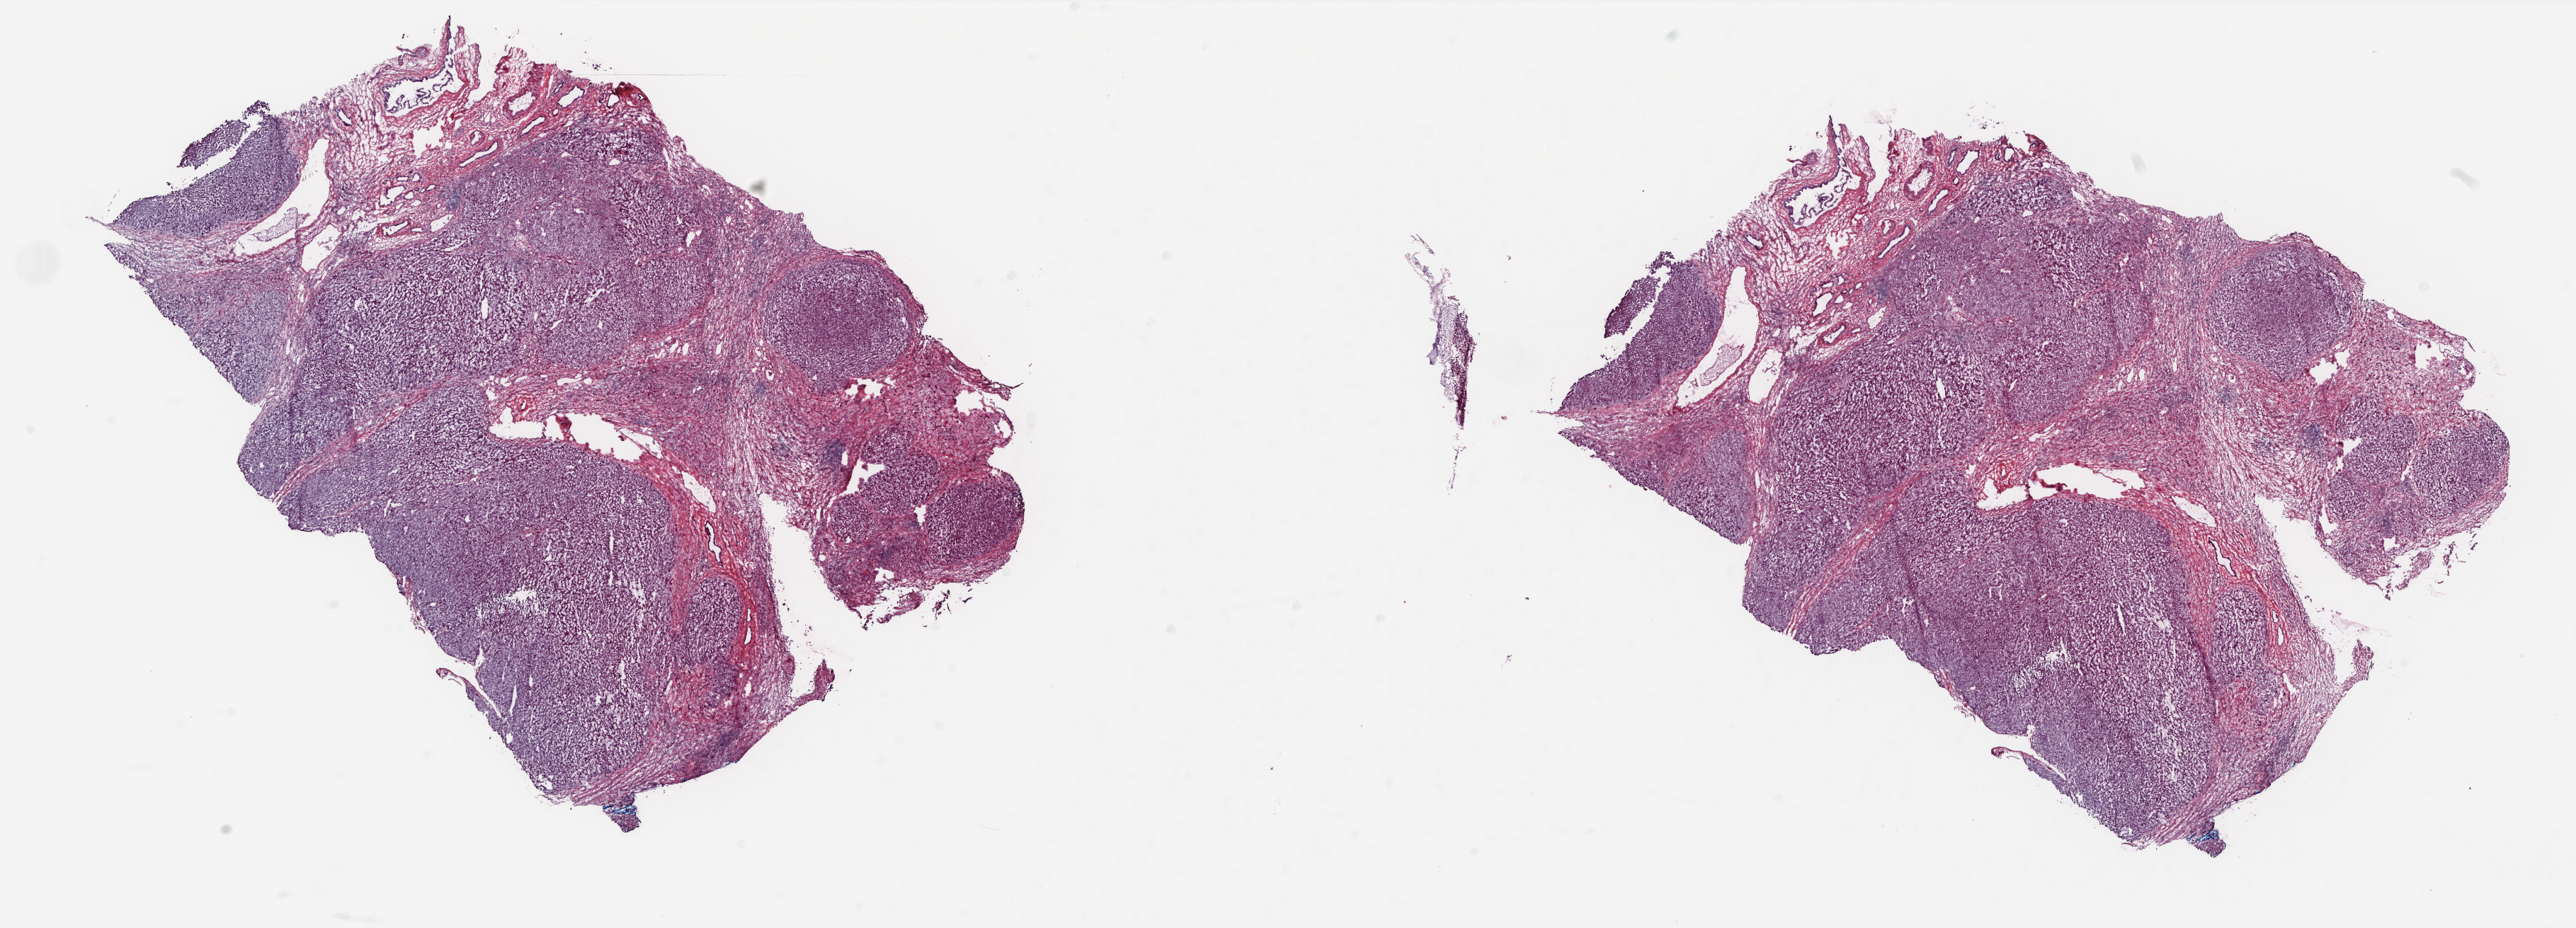
H&E whole-slide image — low-resolution overview of the scanned area, about 29.3 x 10.6 mm (from a 20x scan). Frozen section. Solid tissue normal (non-tumour tissue) sample from the liver. Female, age 79 years at initial diagnosis. Composition of this section per pathologist review: tumour cells 0%, tumour nuclei 0%, normal cells 65%, stromal cells 35%, necrosis 0%. Infiltration values recorded for this section: lymphocyte infiltration 14%, monocyte infiltration 2%, neutrophil infiltration 0%.
- this section: solid tissue normal (non-tumour) sample from the same patient
- patient diagnosis: Hepatocellular carcinoma, NOS